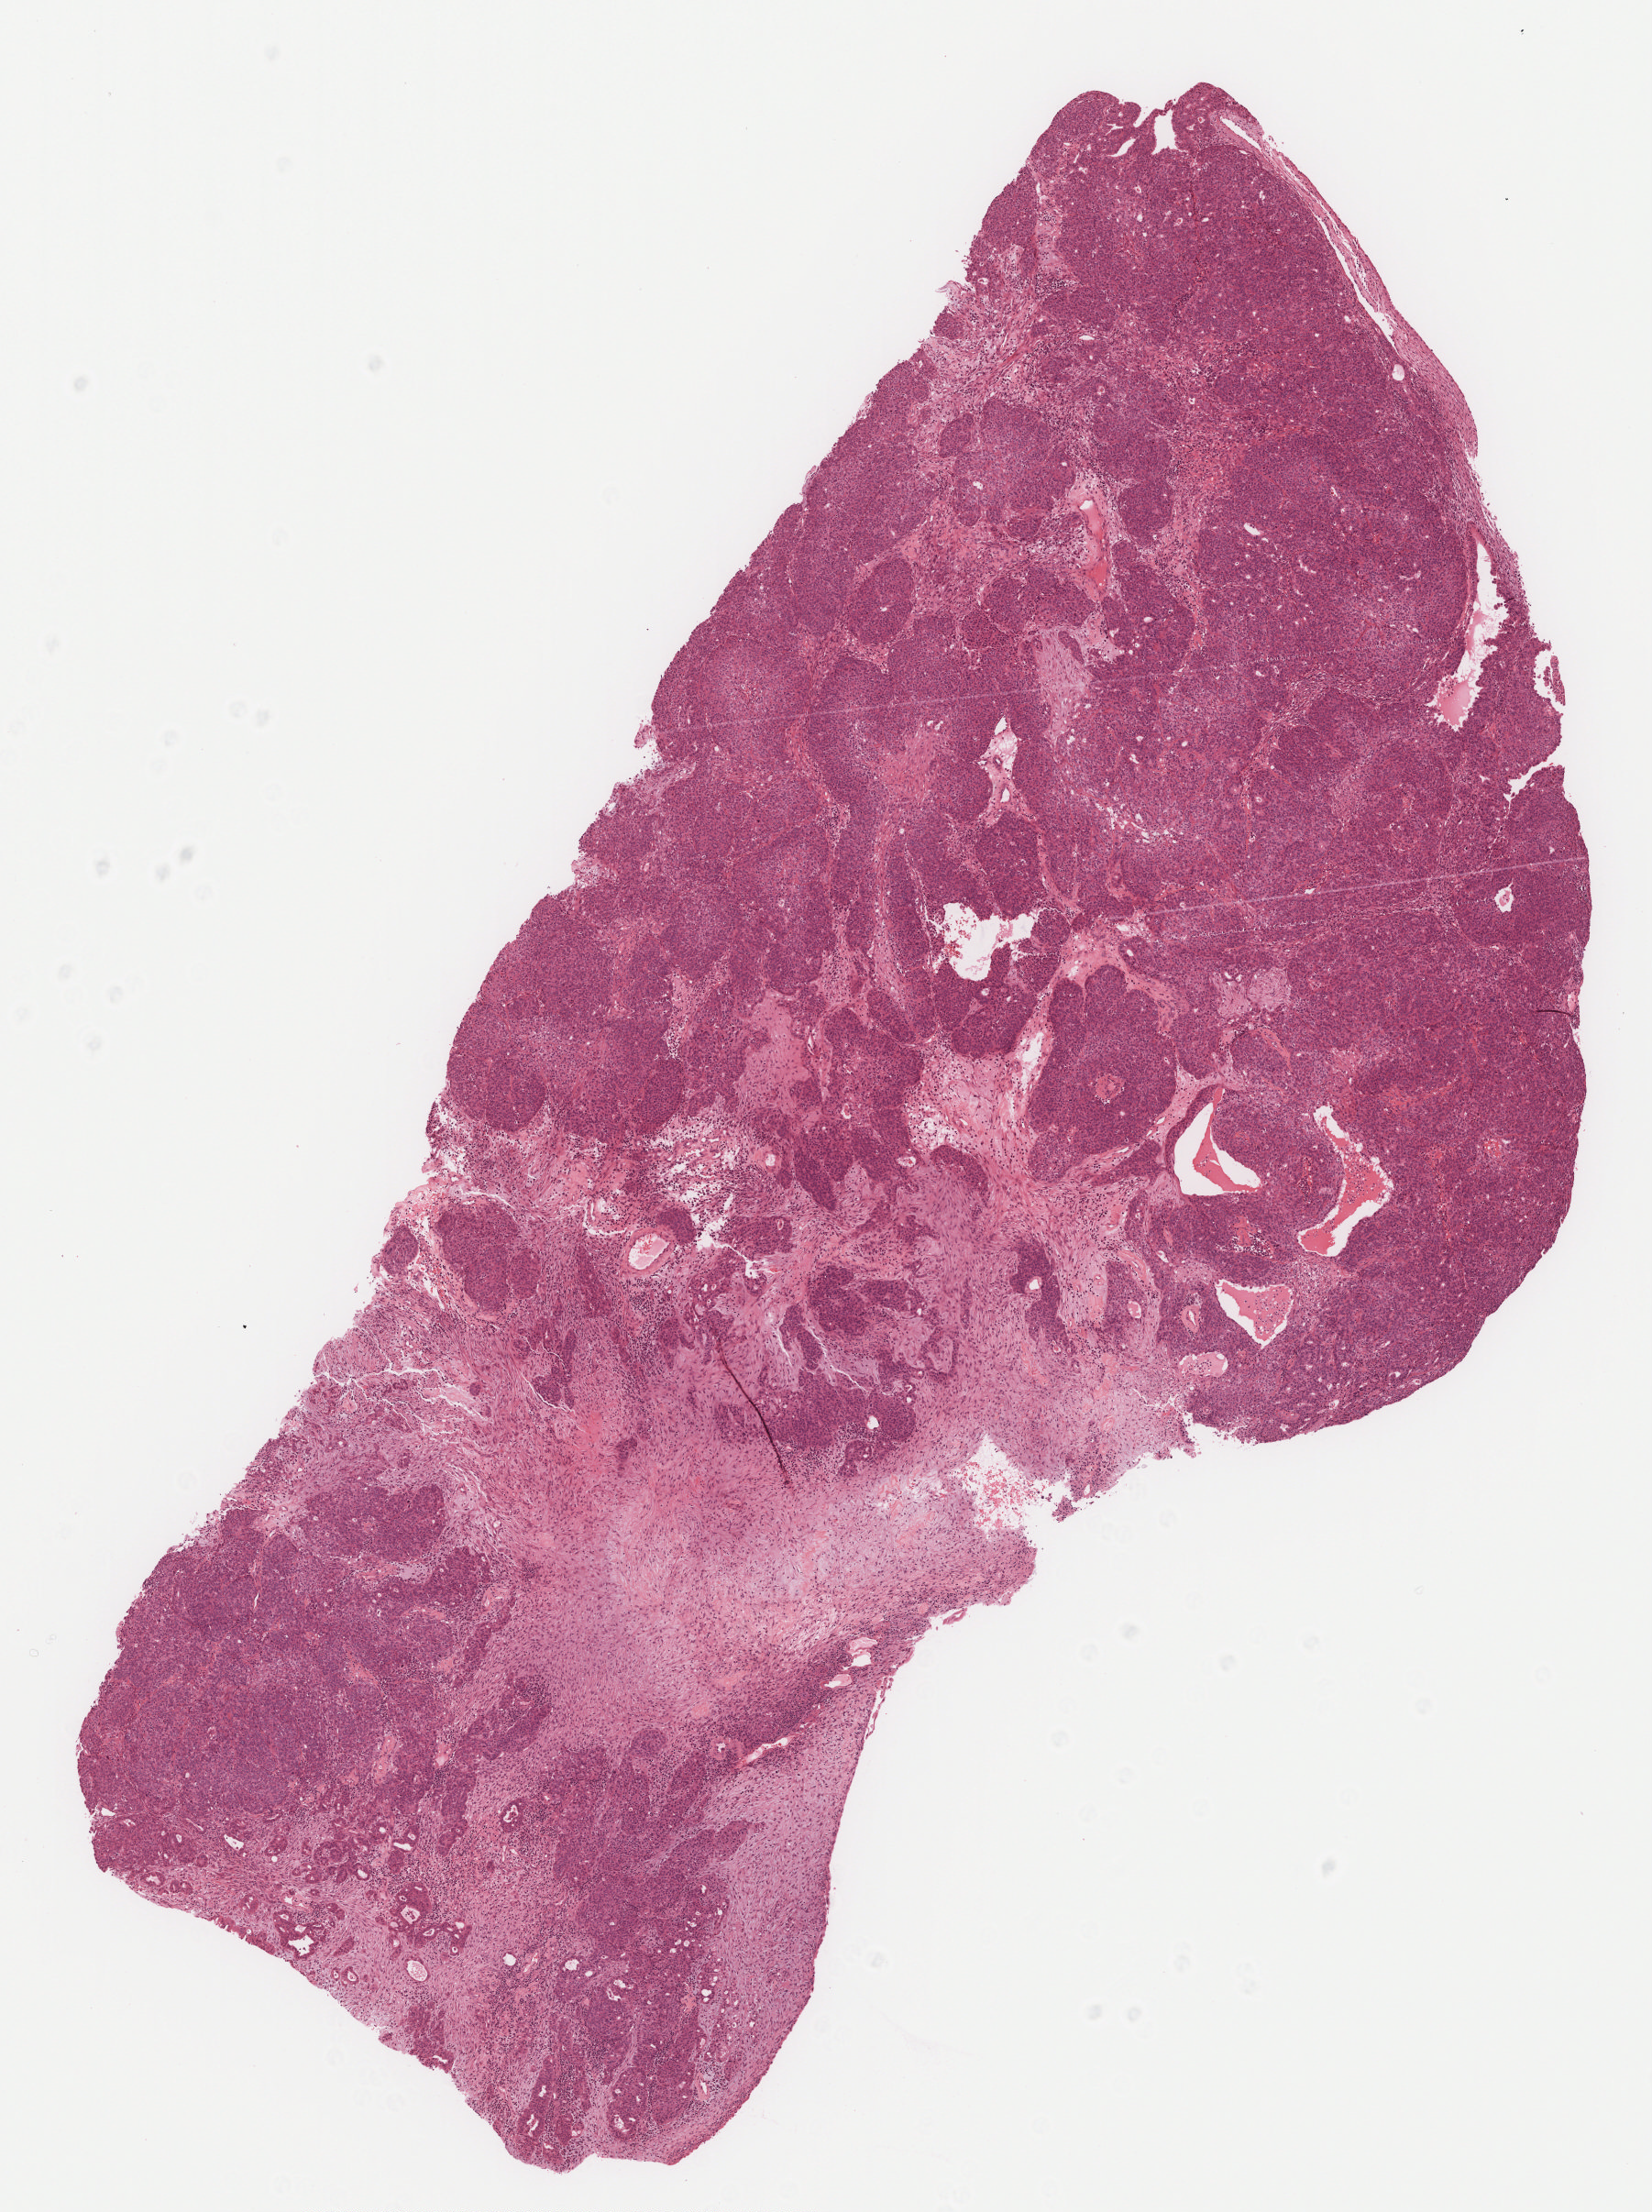
Digitized H&E-stained tissue section (whole slide) — whole scanned area (about 7.3 x 9.7 mm, slide scanned at 40x) shown as a low-resolution overview; formalin-fixed paraffin-embedded (FFPE) diagnostic section; primary tumour sample from the uterus. Female, age 86 years at initial diagnosis. Histologic grade: G3 (poorly differentiated).
- FIGO stage: IA
- pathologic diagnosis: Endometrioid adenocarcinoma, NOS (endometrium)